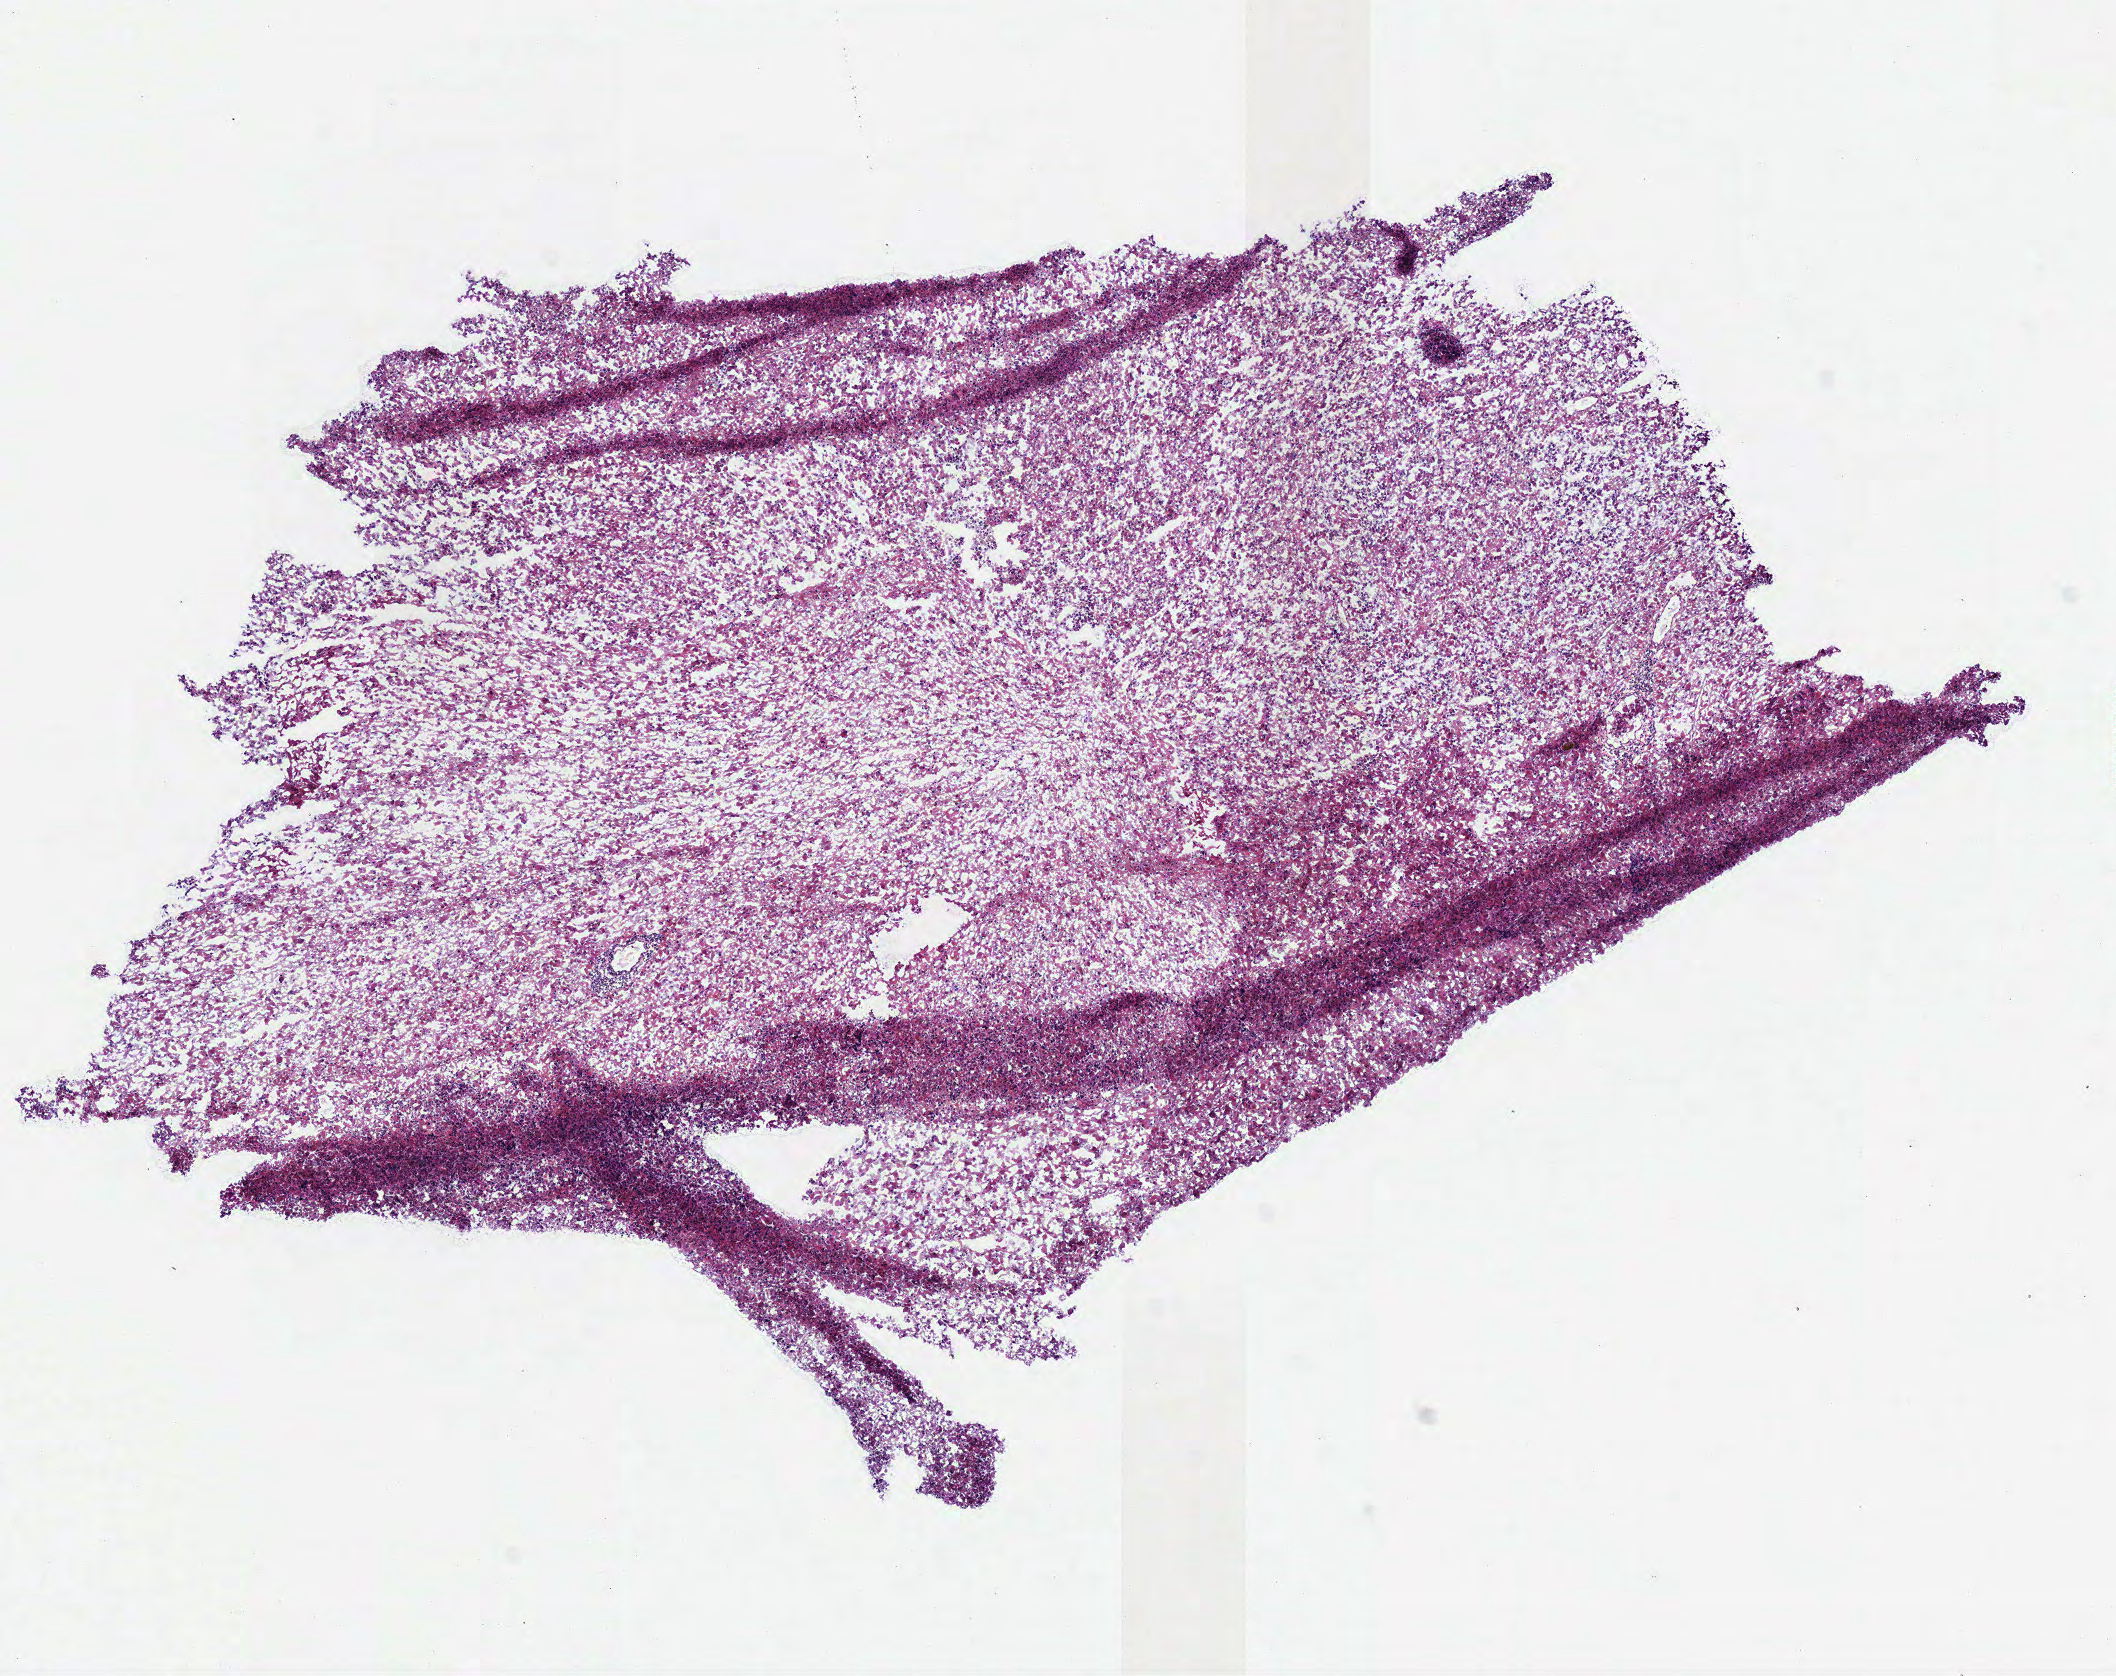
Whole-slide histology image, H&E — shown as a low-resolution overview of the whole scanned area (about 8.3 x 6.6 mm); frozen section; brain, primary tumour sample. Patient: male, age at initial diagnosis 33 years. Histologic grade: G2 (moderately differentiated). Composition of this section per pathologist review: tumour cells 100%, tumour nuclei 75%, normal cells 0%, stromal cells 0%, necrosis 0%.
* laterality: right
* diagnosis: Astrocytoma, NOS (cerebrum)